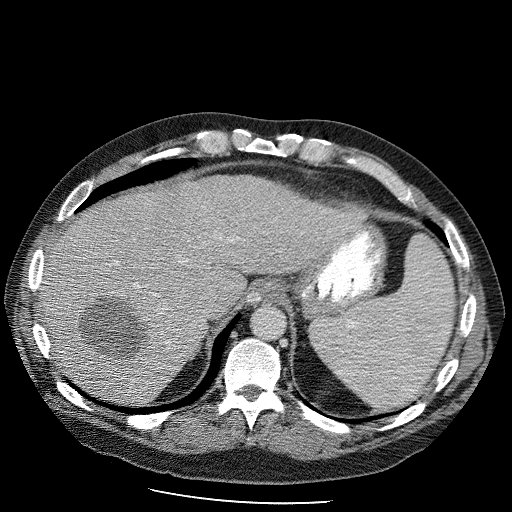
Contrast-enhanced abdominal CT (liver protocol), one axial slice; position 80 of 98 along the scan axis; 120 kVp; soft-tissue window (W 400 / L 40 HU); 2.5 mm slice thickness; 512 × 512 image matrix, field of view 400 × 400 mm. Case-level facts recorded for this patient, not image findings: diagnosis: hepatocellular carcinoma (patient treated with transarterial chemoembolisation; whether this scan precedes or follows treatment is not stated here); TNM stage (as recorded): Stage-II; Child-Pugh class: B.
Annotated regions visible in this slice (semi-automatically segmented with operator editing):
- liver parenchyma outside the tumour (the mass and vessels are separate outlines, so this box may not span the whole liver): bounding box <36,174,362,404> (left, top, right, bottom; pixels)
- mass: <74,292,154,365>
- liver vessels: <197,305,199,307>